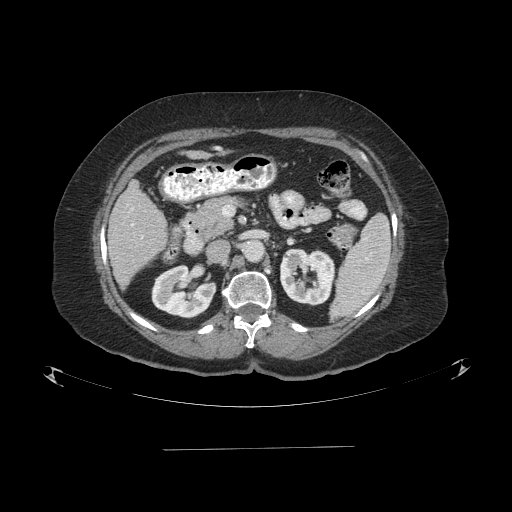
Contrast-enhanced abdominal CT (liver protocol), one axial slice; position 37 of 103 along the scan axis; reconstruction kernel STANDARD; 120 kVp; one of 2 acquisitions stored at this slice position; soft-tissue window (W 400 / L 40 HU); 2.5 mm slice thickness; 512 × 512 image matrix. Case-level facts recorded for this patient, not image findings: diagnosis: hepatocellular carcinoma (patient treated with transarterial chemoembolisation; whether this scan precedes or follows treatment is not stated here); TNM stage (as recorded): Stage-IIIA; Child-Pugh class: A; tumour differentiation: poorly differentiated; tumour nodularity: multinodular.
Annotated regions visible in this slice (semi-automatic segmentation, software-assisted and operator-edited):
- liver parenchyma outside the tumour (the mass and vessels are separate outlines, so this box may not span the whole liver): bounding box [x1, y1, x2, y2] px = [108, 180, 166, 288]
- liver vessels: [131, 208, 143, 238]